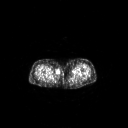
FDG PET of an extremity soft-tissue mass (from a PET/CT study), one axial slice; slice 227 of 311 in the series (ordered by position); 128 × 128 image matrix. Female patient, age 78 years. From the clinical record (not read from this slice): histological type: leiomyosarcoma; grade: intermediate; site of the primary tumour: parascapusular.
Outlined on this slice (expert contour drawn on MRI and transferred to this co-registered scan by the dataset authors):
- gross tumour volume including surrounding oedema: bounding box <55,71,60,74> (left, top, right, bottom; pixels)
- gross tumour volume (mass): <56,71,59,74>